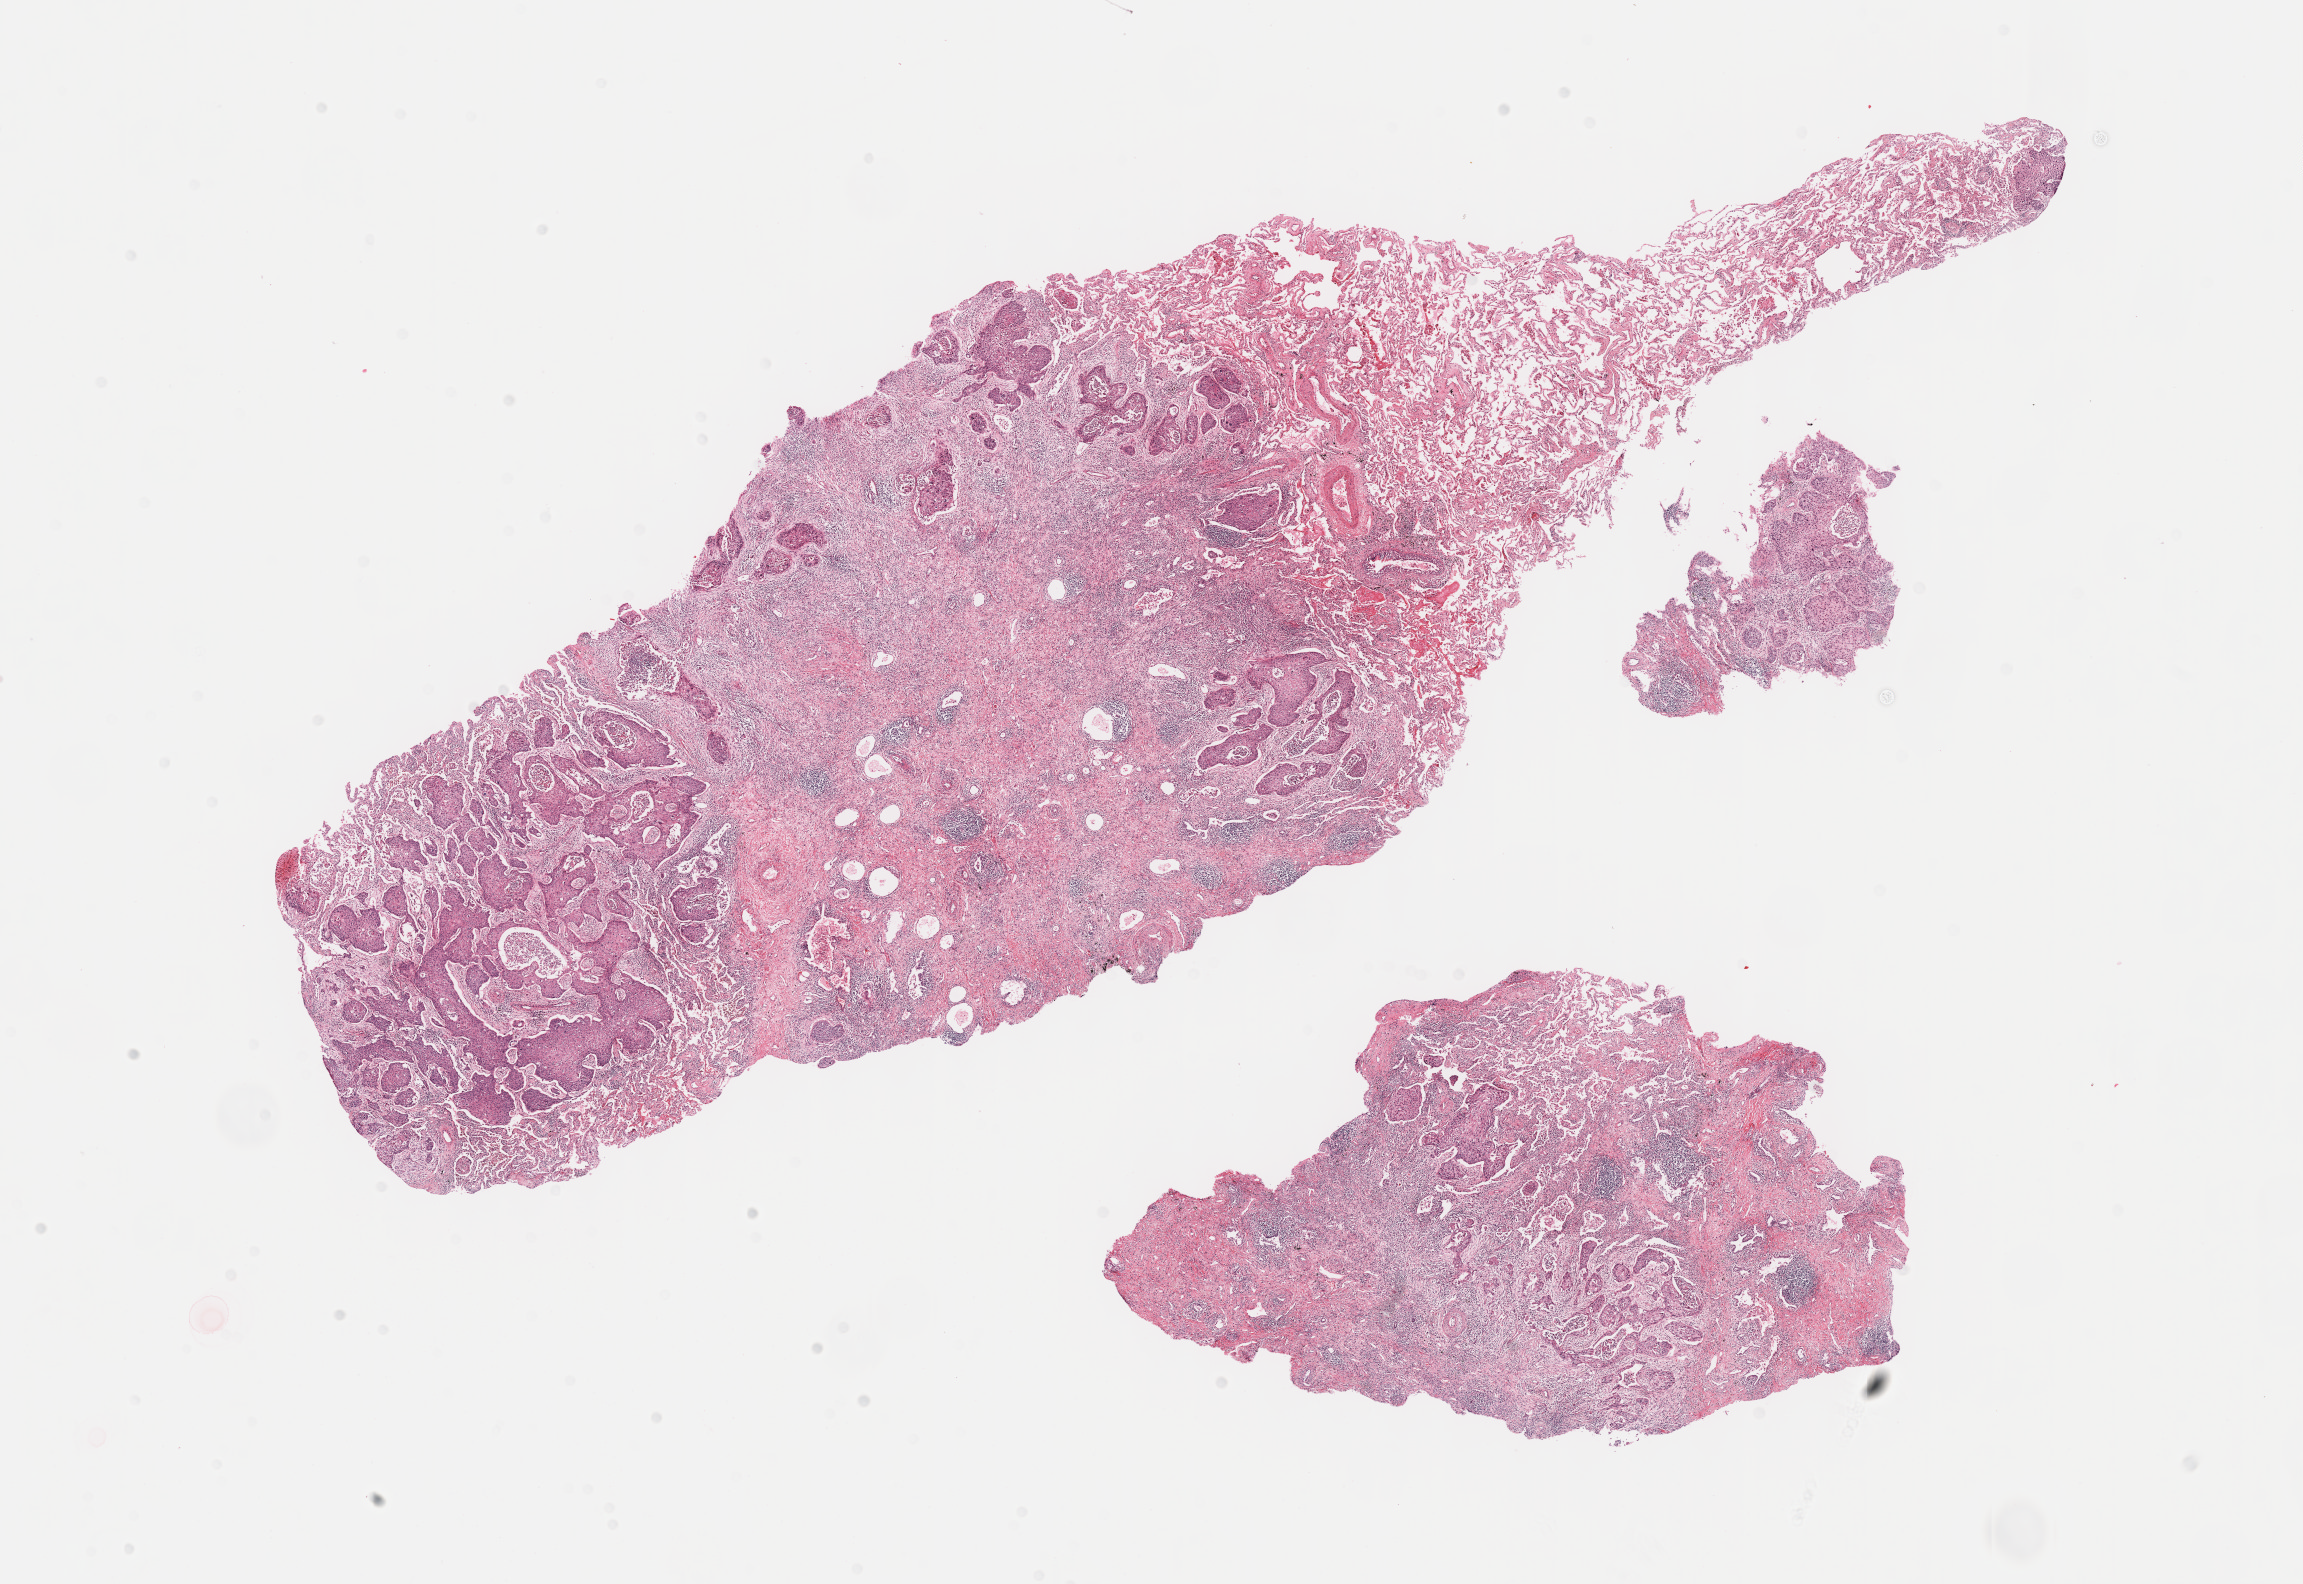
Whole-slide histology image, H&E-stained — whole scanned area (about 18.6 x 12.8 mm, acquisition: 40x scan) shown as a low-resolution overview. FFPE section. Sample: primary tumour, lung. Female patient; age at initial diagnosis 80 years.
Pathologic diagnosis: Squamous cell carcinoma, NOS (upper lobe, lung). AJCC pathologic stage: IB (6th edition).